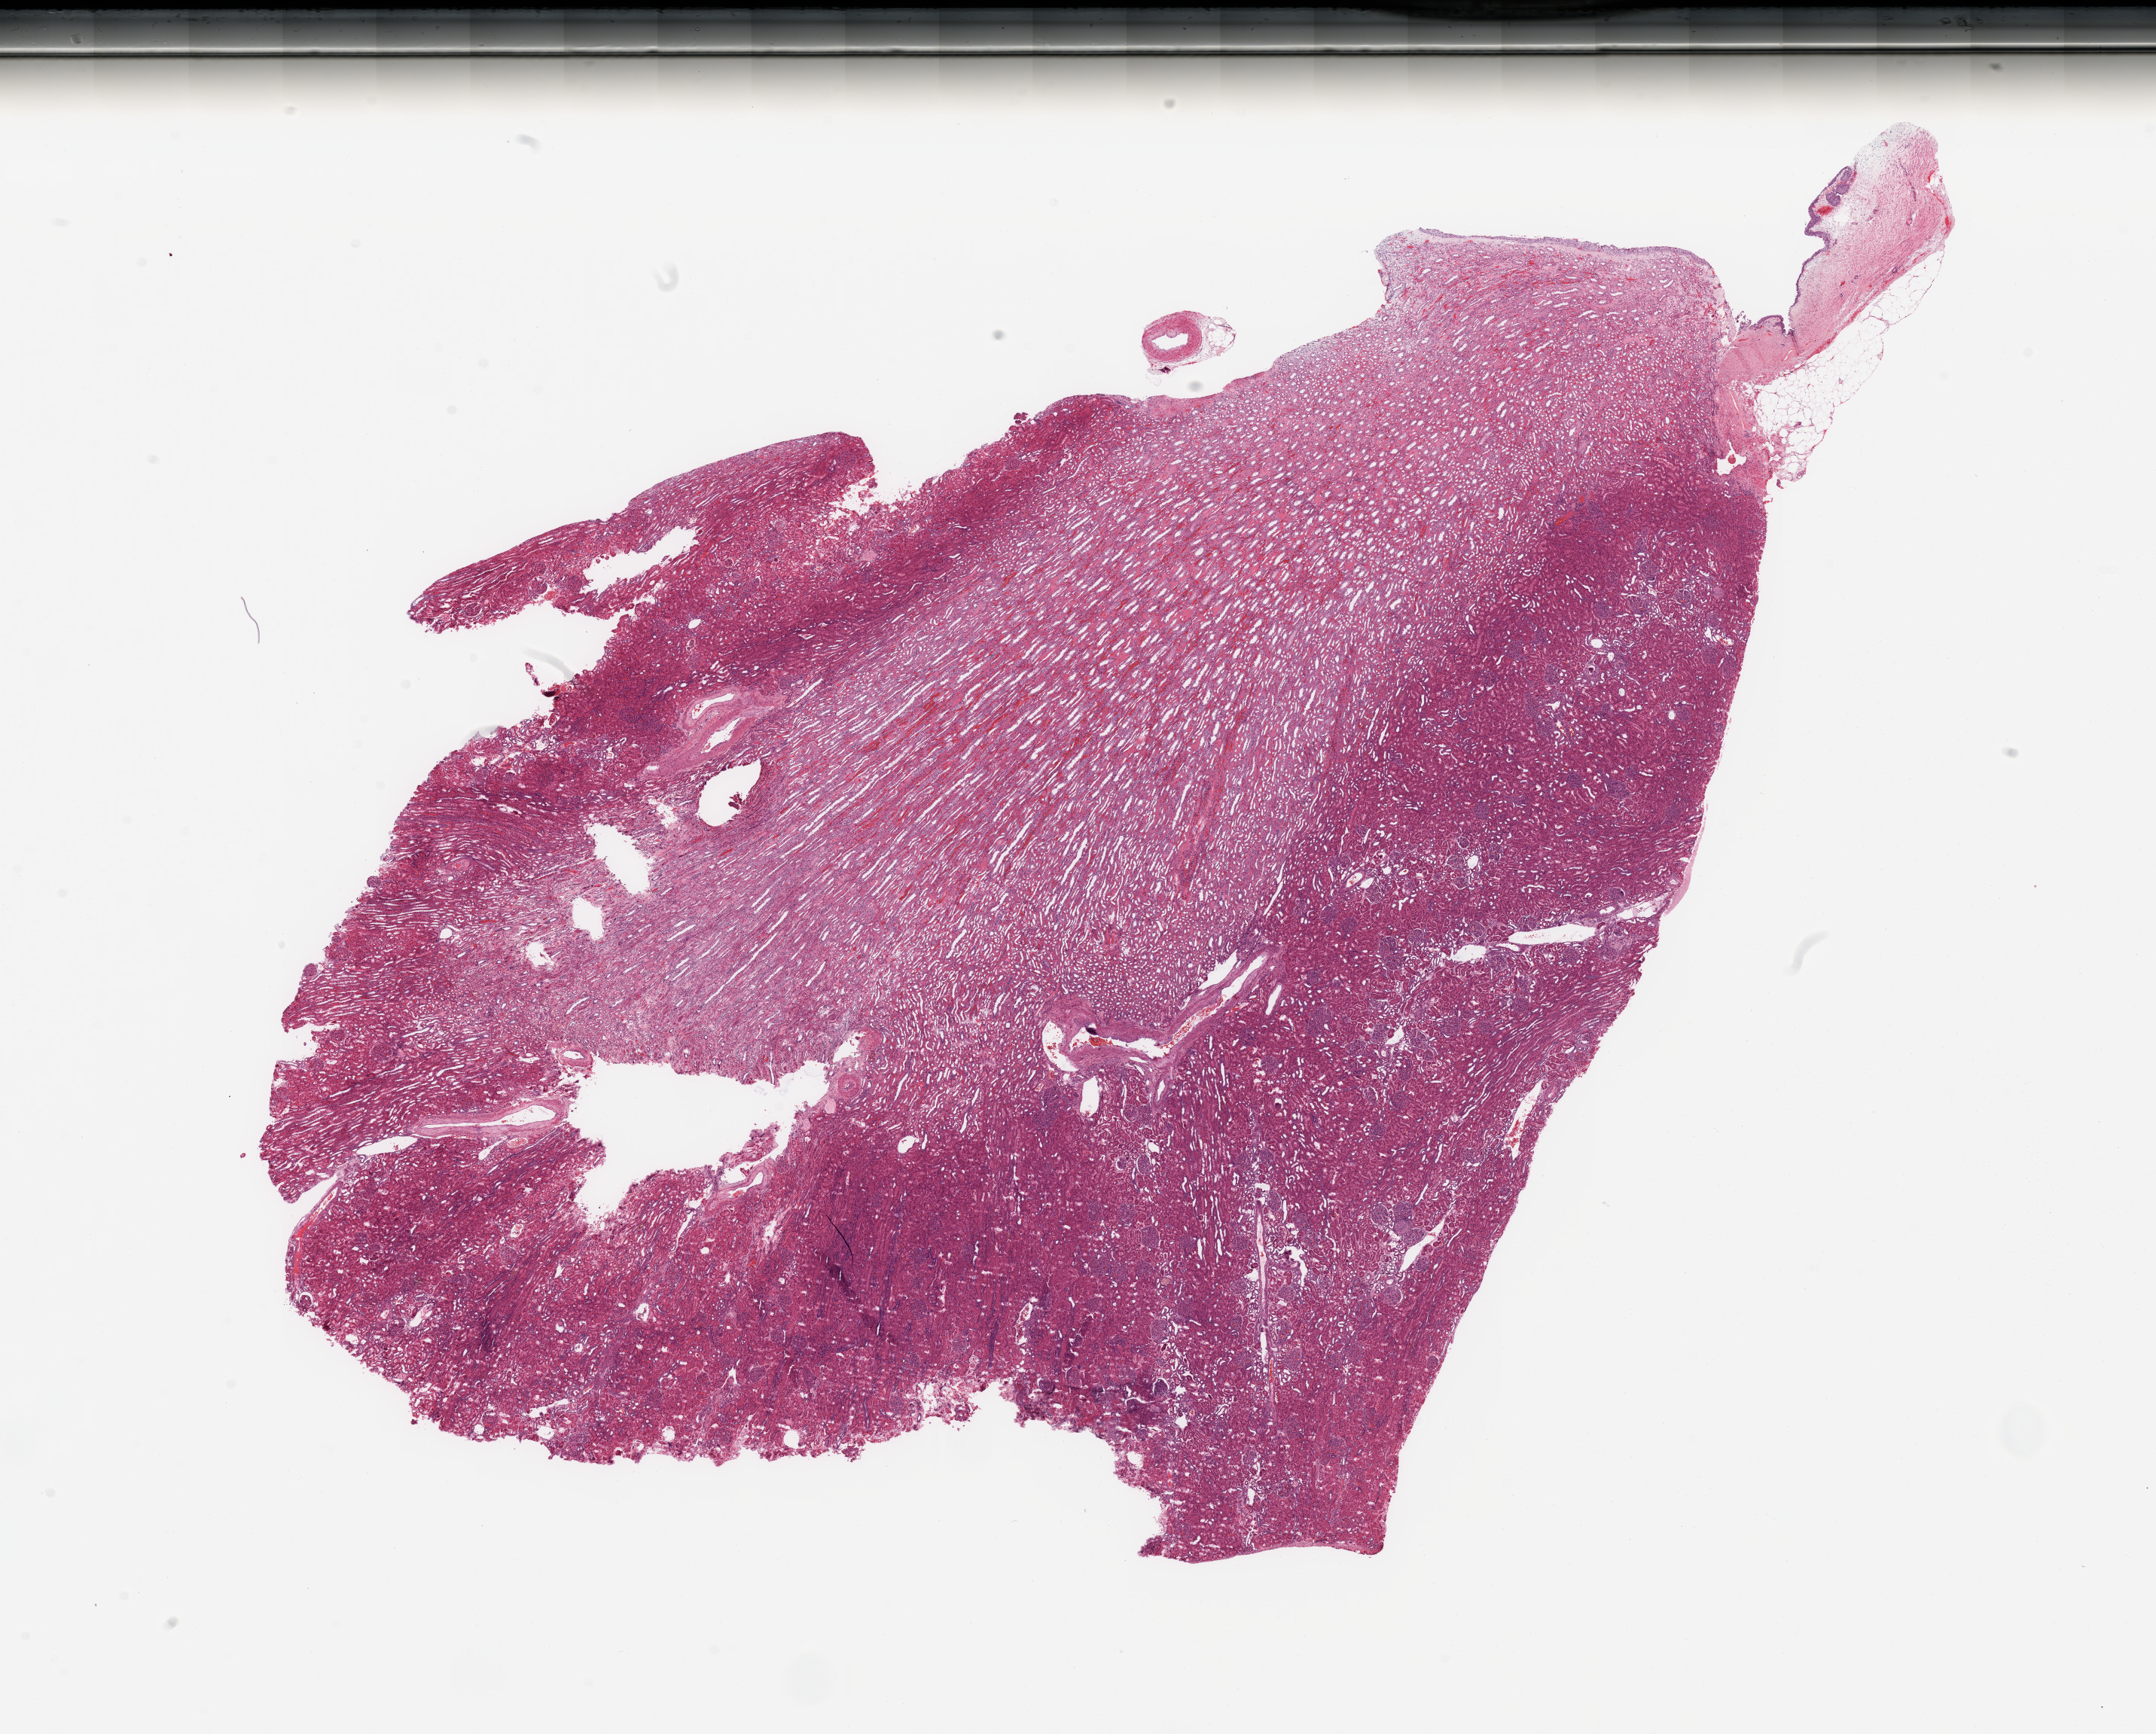
Whole-slide histology image, H&E-stained — a low-resolution overview of the entire scanned area, about 22.6 x 18.2 mm; normal (non-tumour) tissue sample, sampled site: kidney. Male, 47 y/o.
• this section: normal (non-tumour) tissue from the same patient
• patient diagnosis: Renal cell carcinoma, NOS